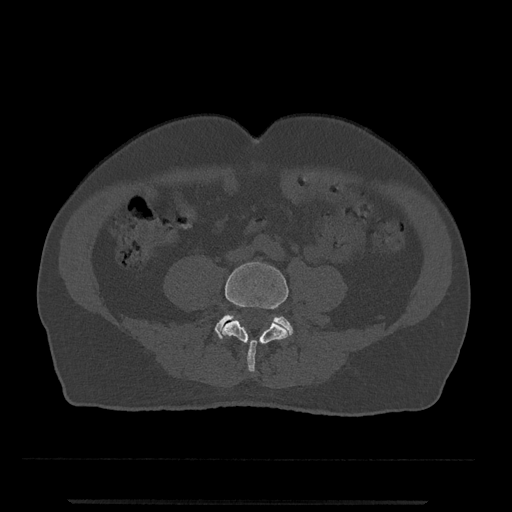
CT including the spine, one axial slice. Slice 116 of 797 in the series (ordered by position). Bone window (W 1800 / L 400 HU). 0.5 mm slice thickness. 512 × 512 image matrix, field of view 419 × 419 mm. Male patient, age 63 years. Case-level facts recorded for this patient, not image findings: primary cancer: prostate.
Structures marked on this image (semi-automatic segmentation, software-assisted and operator-edited):
- L4 vertebra: bounding box [x1, y1, x2, y2] px = [222, 262, 288, 372]
- L5 vertebra: [215, 314, 293, 338]